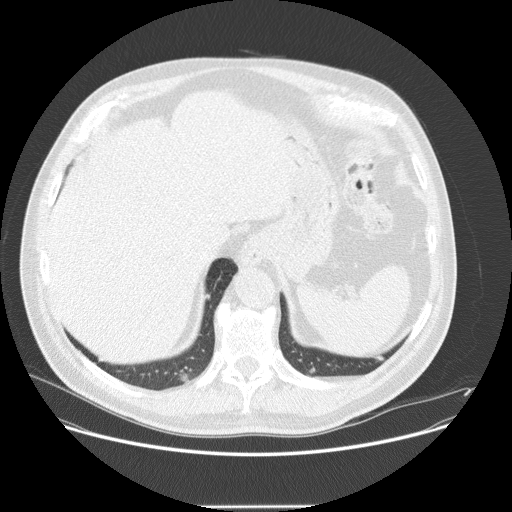
Low-dose screening chest CT, axial slice, first (baseline) screen, lung window (W 1500 / L -600 HU), 2.5 mm slice thickness, 120 kVp. Male, age 61 years at enrolment.
Lesion marked by an expert reader, box from (x=161, y=364) to (x=202, y=401) px. The screening reader recorded 2 non-calcified nodules or masses ≥4 mm on this exam (left lower lobe, right lower lobe); which of them this box marks is not recorded. Official screen result: positive, change unspecified: nodule(s) >= 4 mm or enlarging nodule(s), mass(es), or other non-specific abnormalities suspicious for lung cancer. Later outcome: lung cancer diagnosed 41 days after this screen — bronchiolo-alveolar carcinoma, mucinous, right lower lobe, well differentiated (G1), stage IV (AJCC 6th edition), 23 mm at pathology.